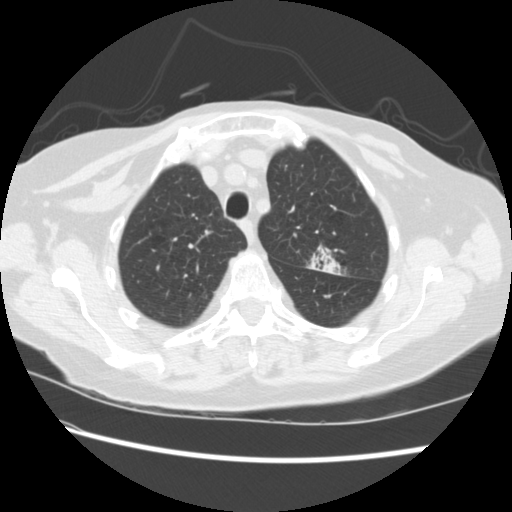
Low-dose screening chest CT, axial slice, first (baseline) screen, lung window (W 1500 / L -600 HU), standard (soft-tissue) reconstruction kernel (STANDARD), slice 51 of 224 in the series. Female, age 74 years at enrolment. Former smoker at enrolment.
Expert reader's lesion annotation, bounding box (x1, y1, x2, y2) in pixels: (297, 239, 347, 281). The screening reader recorded 2 non-calcified nodules or masses ≥4 mm on this exam; which of them this box marks is not recorded. Official screen result: positive, change unspecified: nodule(s) >= 4 mm or enlarging nodule(s), mass(es), or other non-specific abnormalities suspicious for lung cancer. Later outcome: lung cancer diagnosed 309 days after this screen — non-small cell carcinoma, left upper lobe, stage IV (AJCC 6th edition).